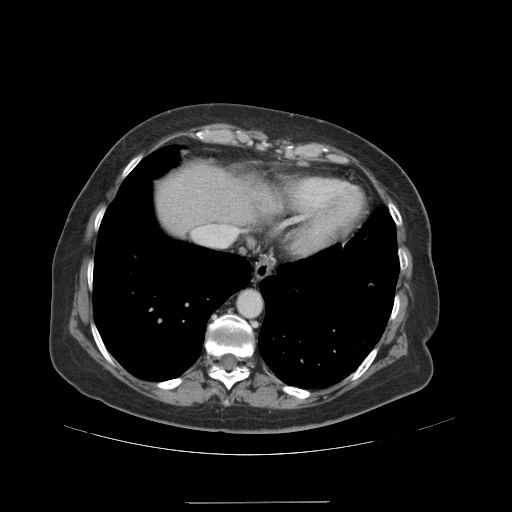
Contrast-enhanced abdominal CT (liver protocol), one axial slice. Position 86 of 99 along the scan axis. 140 kVp. Soft-tissue window (W 400 / L 40 HU). 2.5 mm slice thickness. 512 × 512 image matrix, field of view 440 × 440 mm. Case-level facts recorded for this patient, not image findings: diagnosis: hepatocellular carcinoma (patient treated with transarterial chemoembolisation; whether this scan precedes or follows treatment is not stated here); TNM stage (as recorded): Stage-IVA.
Outlined on this slice (semi-automatically segmented with operator editing):
- abdominal aorta: box from (x=238, y=291) to (x=260, y=317) px
- liver parenchyma outside the tumour (the mass and vessels are separate outlines, so this box may not span the whole liver): (x=156, y=165)–(x=278, y=234)